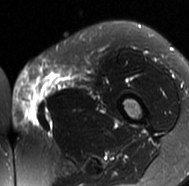
MRI of an extremity soft-tissue mass, one axial slice. Slice 24 of 77 in the series (ordered by position). T2-weighted fat-saturated. MR volume resampled by the dataset authors to the PET/CT grid (not the native acquisition matrix). 3.27 mm slice thickness. 189 × 186 image matrix, field of view 185 × 182 mm. Female patient. From the clinical record (not read from this slice): histological type: leiomyosarcoma; grade: high; site of the primary tumour: groin.
Structures marked on this image (expert contour drawn on MRI and transferred to this co-registered scan by the dataset authors):
- gross tumour volume including surrounding oedema: bounding box (x1, y1, x2, y2) in pixels: (10, 61, 93, 131)